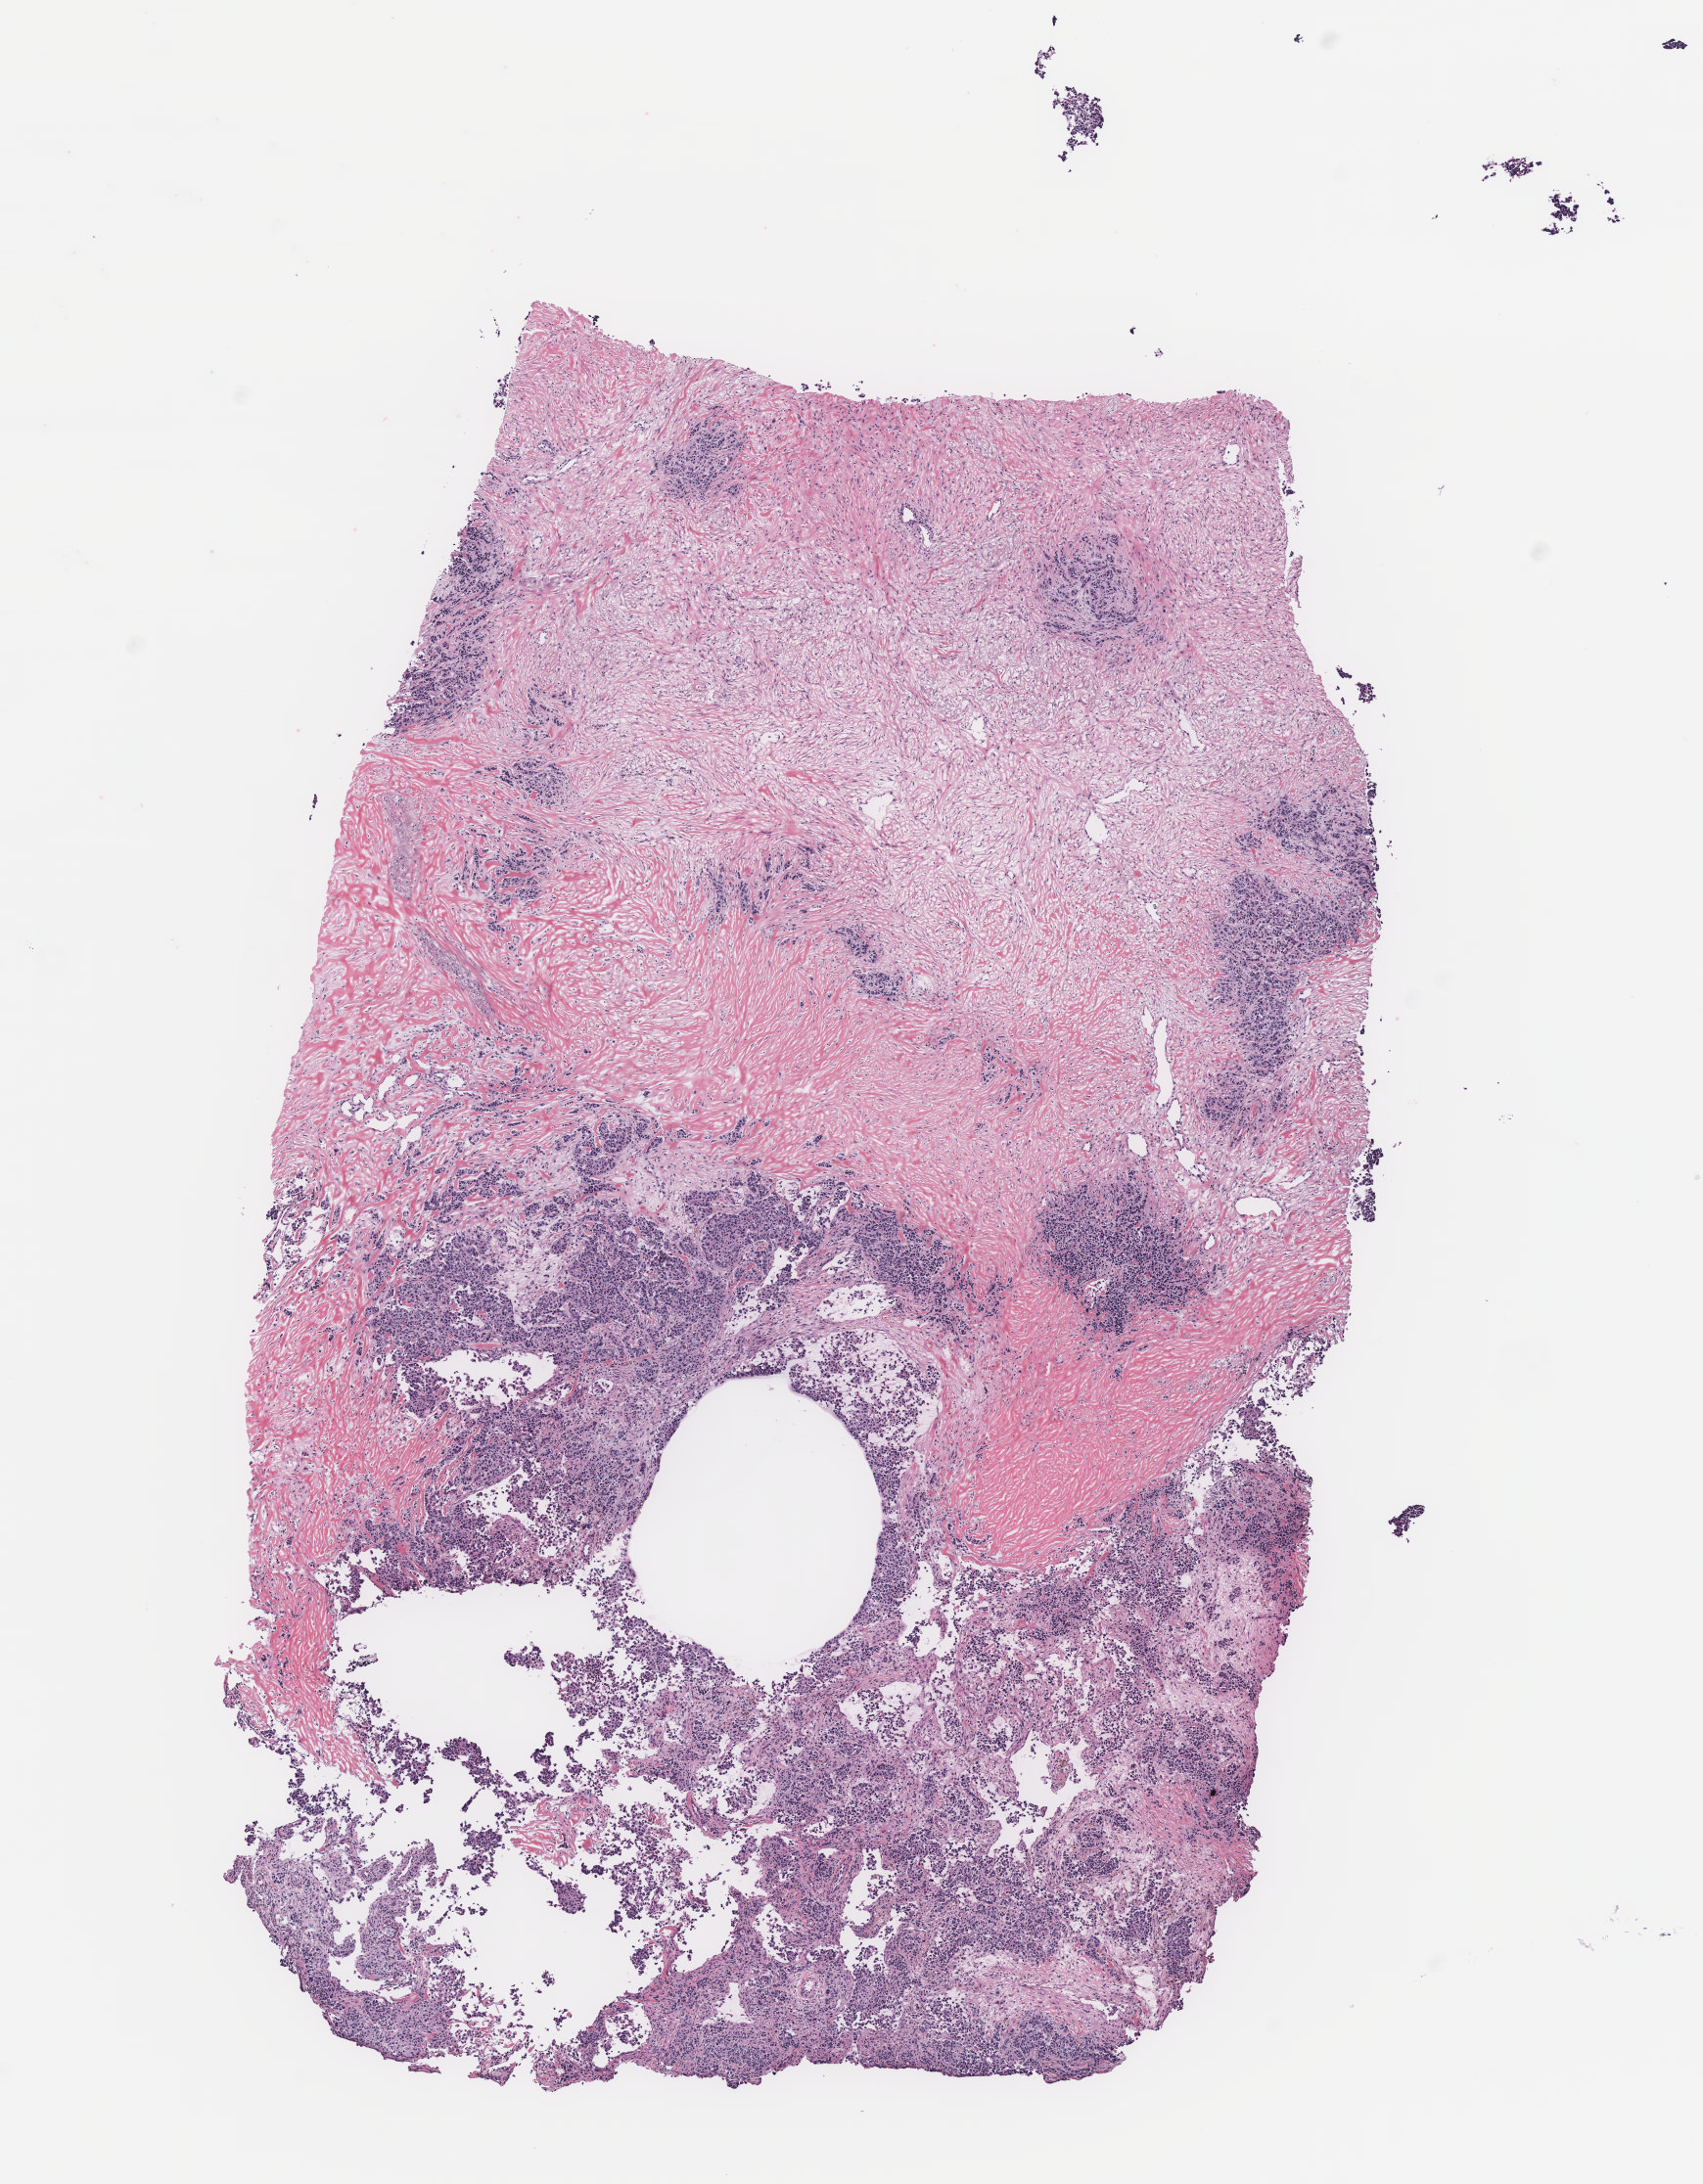
Whole-slide histology image, Hematoxylin and eosin (H&E) stained, low-resolution overview of the scanned area, about 7.0 x 8.9 mm; breast, tumour tissue. Female, 75 y/o.
* histologic diagnosis: Infiltrating duct carcinoma, NOS
* AJCC pathologic stage: IIIB